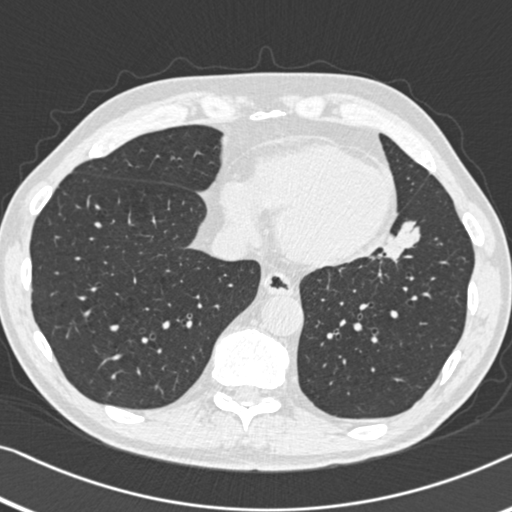
Low-dose screening chest CT, one axial slice; slice 138 of 383 in the series (ordered by position); reconstruction kernel B30f; lung window (W 1500 / L -600 HU); 1 mm slice thickness; 512 × 512 image matrix.
Outlined on this slice (outlined manually by an expert reader):
- lesion 1 (tumor, upper lobe of left lung): bounding box [x1, y1, x2, y2] px = [382, 221, 420, 262]